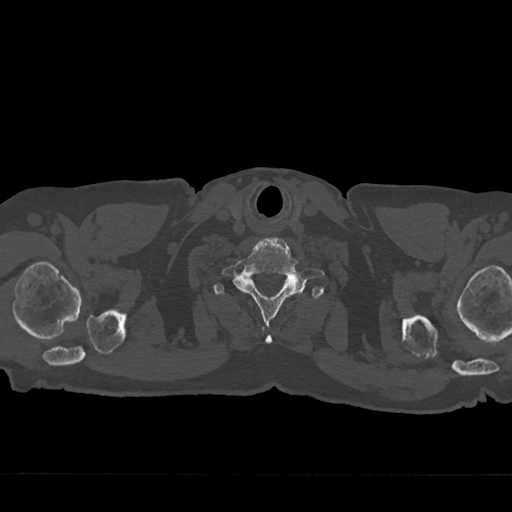
CT including the spine, one axial slice. Position 688 of 797 along the scan axis. Reconstruction kernel Br40s/3. Bone window (W 1800 / L 400 HU). 0.5 mm slice thickness. 512 × 512 image matrix, field of view 377 × 377 mm. Male patient, age 75 years. From the clinical record (not read from this slice): primary cancer: renal.
Annotated regions visible in this slice (semi-automatically segmented with operator editing):
- T1 vertebra: box from (x=214, y=283) to (x=302, y=295) px